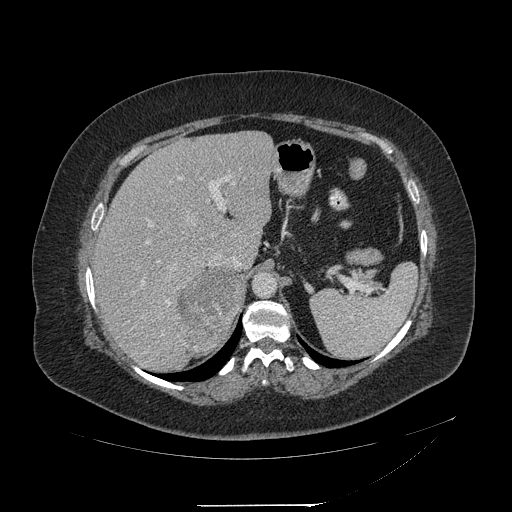
Contrast-enhanced abdominal CT, one axial slice; reconstruction kernel STANDARD; 120 kVp; intravenous contrast given; soft-tissue window (W 400 / L 40 HU); 1.25 mm slice thickness; 512 × 512 image matrix, field of view 453 × 453 mm. Female patient, age 55 years. Case-level facts recorded for this patient, not image findings: diagnosis: adrenocortical carcinoma; tumour side: right adrenal; tumour size at pathology: 11 cm; Ki-67 index: 20 %; stage (as recorded): 2.
Outlined on this slice (semi-automatically segmented with operator editing):
- mass: bounding box [x1, y1, x2, y2] px = [178, 267, 243, 351]